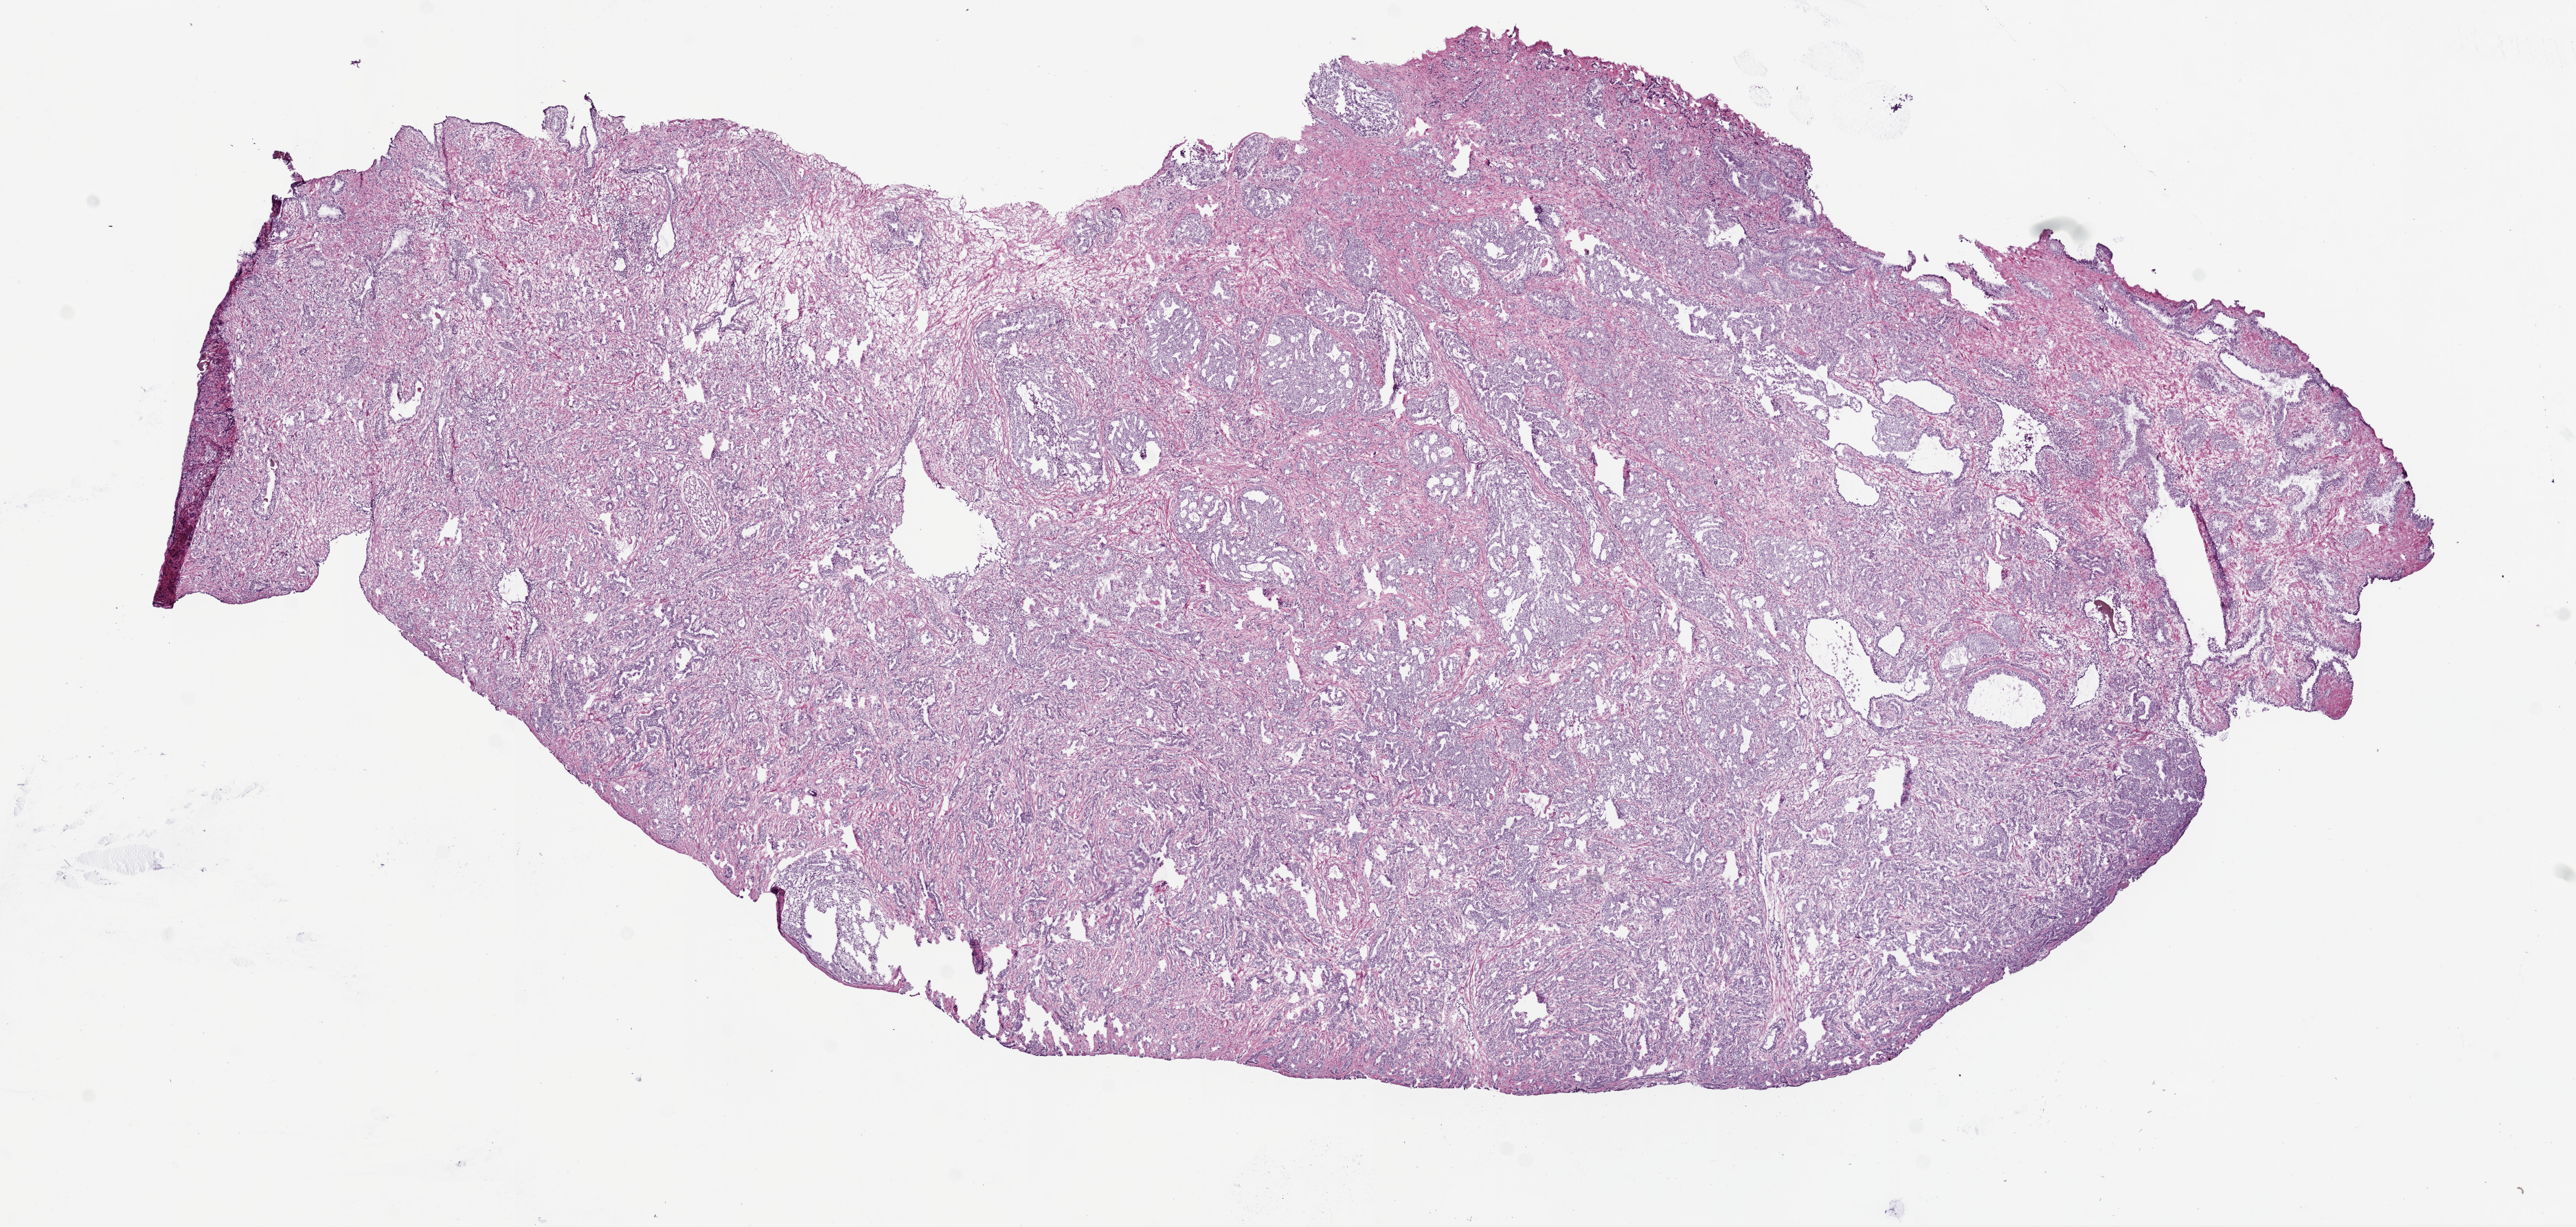
Whole-slide histology image, H&E — low-resolution overview of the scanned area, about 15.0 x 7.2 mm (from a 20x scan); frozen section; sample: primary tumour, prostate. Male, age 69 years at initial diagnosis. Gleason score: 7 (4+3). Pathologist review of this section (percent, as recorded): tumour cells 70%, tumour nuclei 75%, normal cells 10%, stromal cells 20%, necrosis 0%. Inflammatory infiltration, as recorded: lymphocyte infiltration 0%, monocyte infiltration 0%, neutrophil infiltration 0%.
• lymph nodes positive (case pathology): 0 of 9 examined
• pathologic diagnosis: Acinar cell carcinoma (prostate gland)
• laterality: bilateral